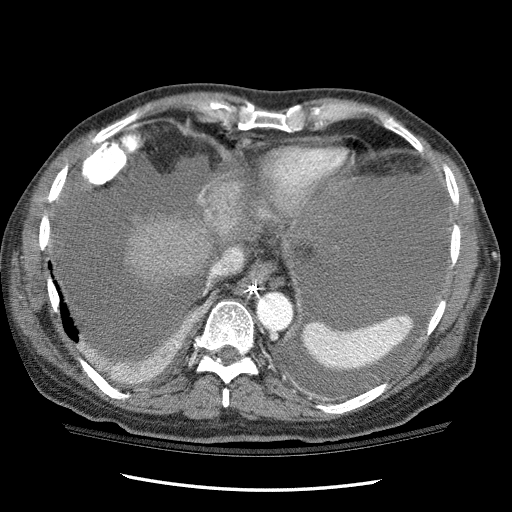
Contrast-enhanced abdominal CT (liver protocol), one axial slice; slice 95 of 114 in the series (ordered by position); 120 kVp; one of 3 acquisitions stored at this slice position; soft-tissue window (W 400 / L 40 HU); 2.5 mm slice thickness; 512 × 512 image matrix. Case-level facts recorded for this patient, not image findings: diagnosis: hepatocellular carcinoma (patient treated with transarterial chemoembolisation; whether this scan precedes or follows treatment is not stated here); TNM stage (as recorded): Stage-I; Child-Pugh class: C; tumour nodularity: uninodular.
Outlined on this slice (semi-automatically segmented with operator editing):
- liver parenchyma outside the tumour (the mass and vessels are separate outlines, so this box may not span the whole liver): bounding box (x1, y1, x2, y2) in pixels: (122, 170, 270, 285)
- mass: (204, 179, 244, 236)